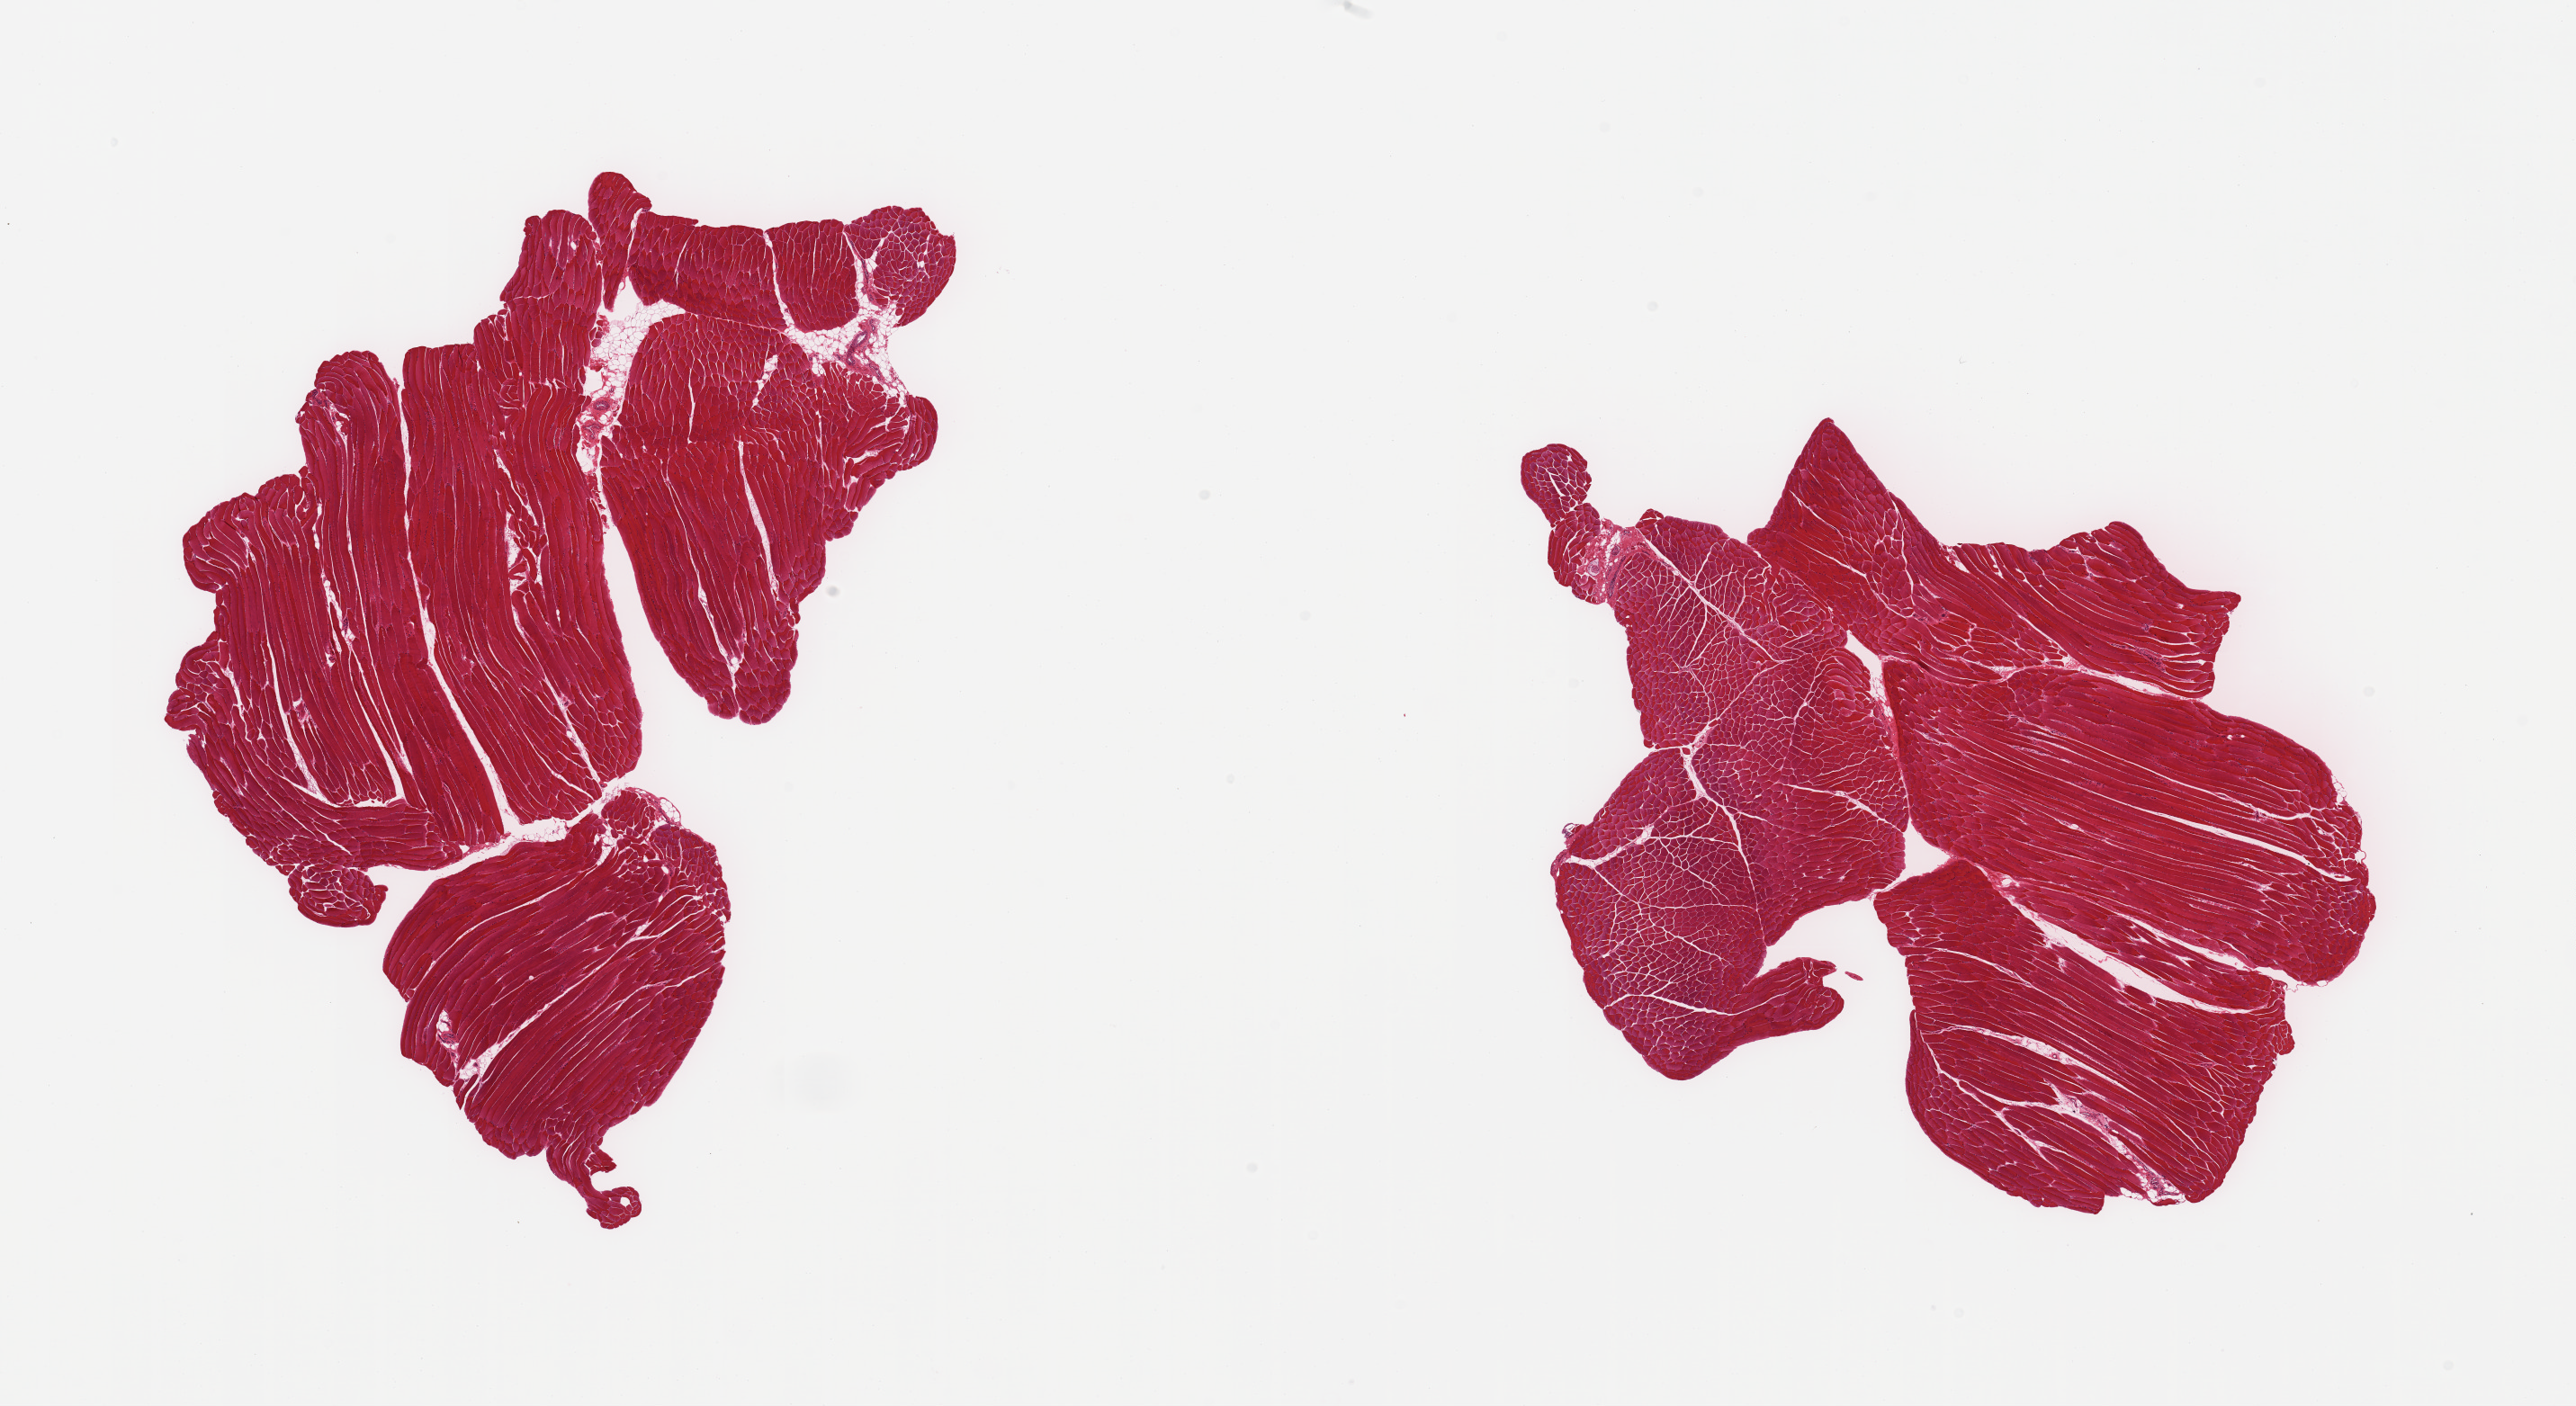
Digitized haematoxylin and eosin-stained section, brightfield, shown as a low-resolution overview of the whole scanned area (about 22.6 x 12.4 mm). PAXgene-fixed, paraffin-embedded tissue. Target tissue: skeletal muscle. Tissue donor sample. Donor: male.
- review note (as recorded): 2 pieces; well trimmed skeletal muscle fibers